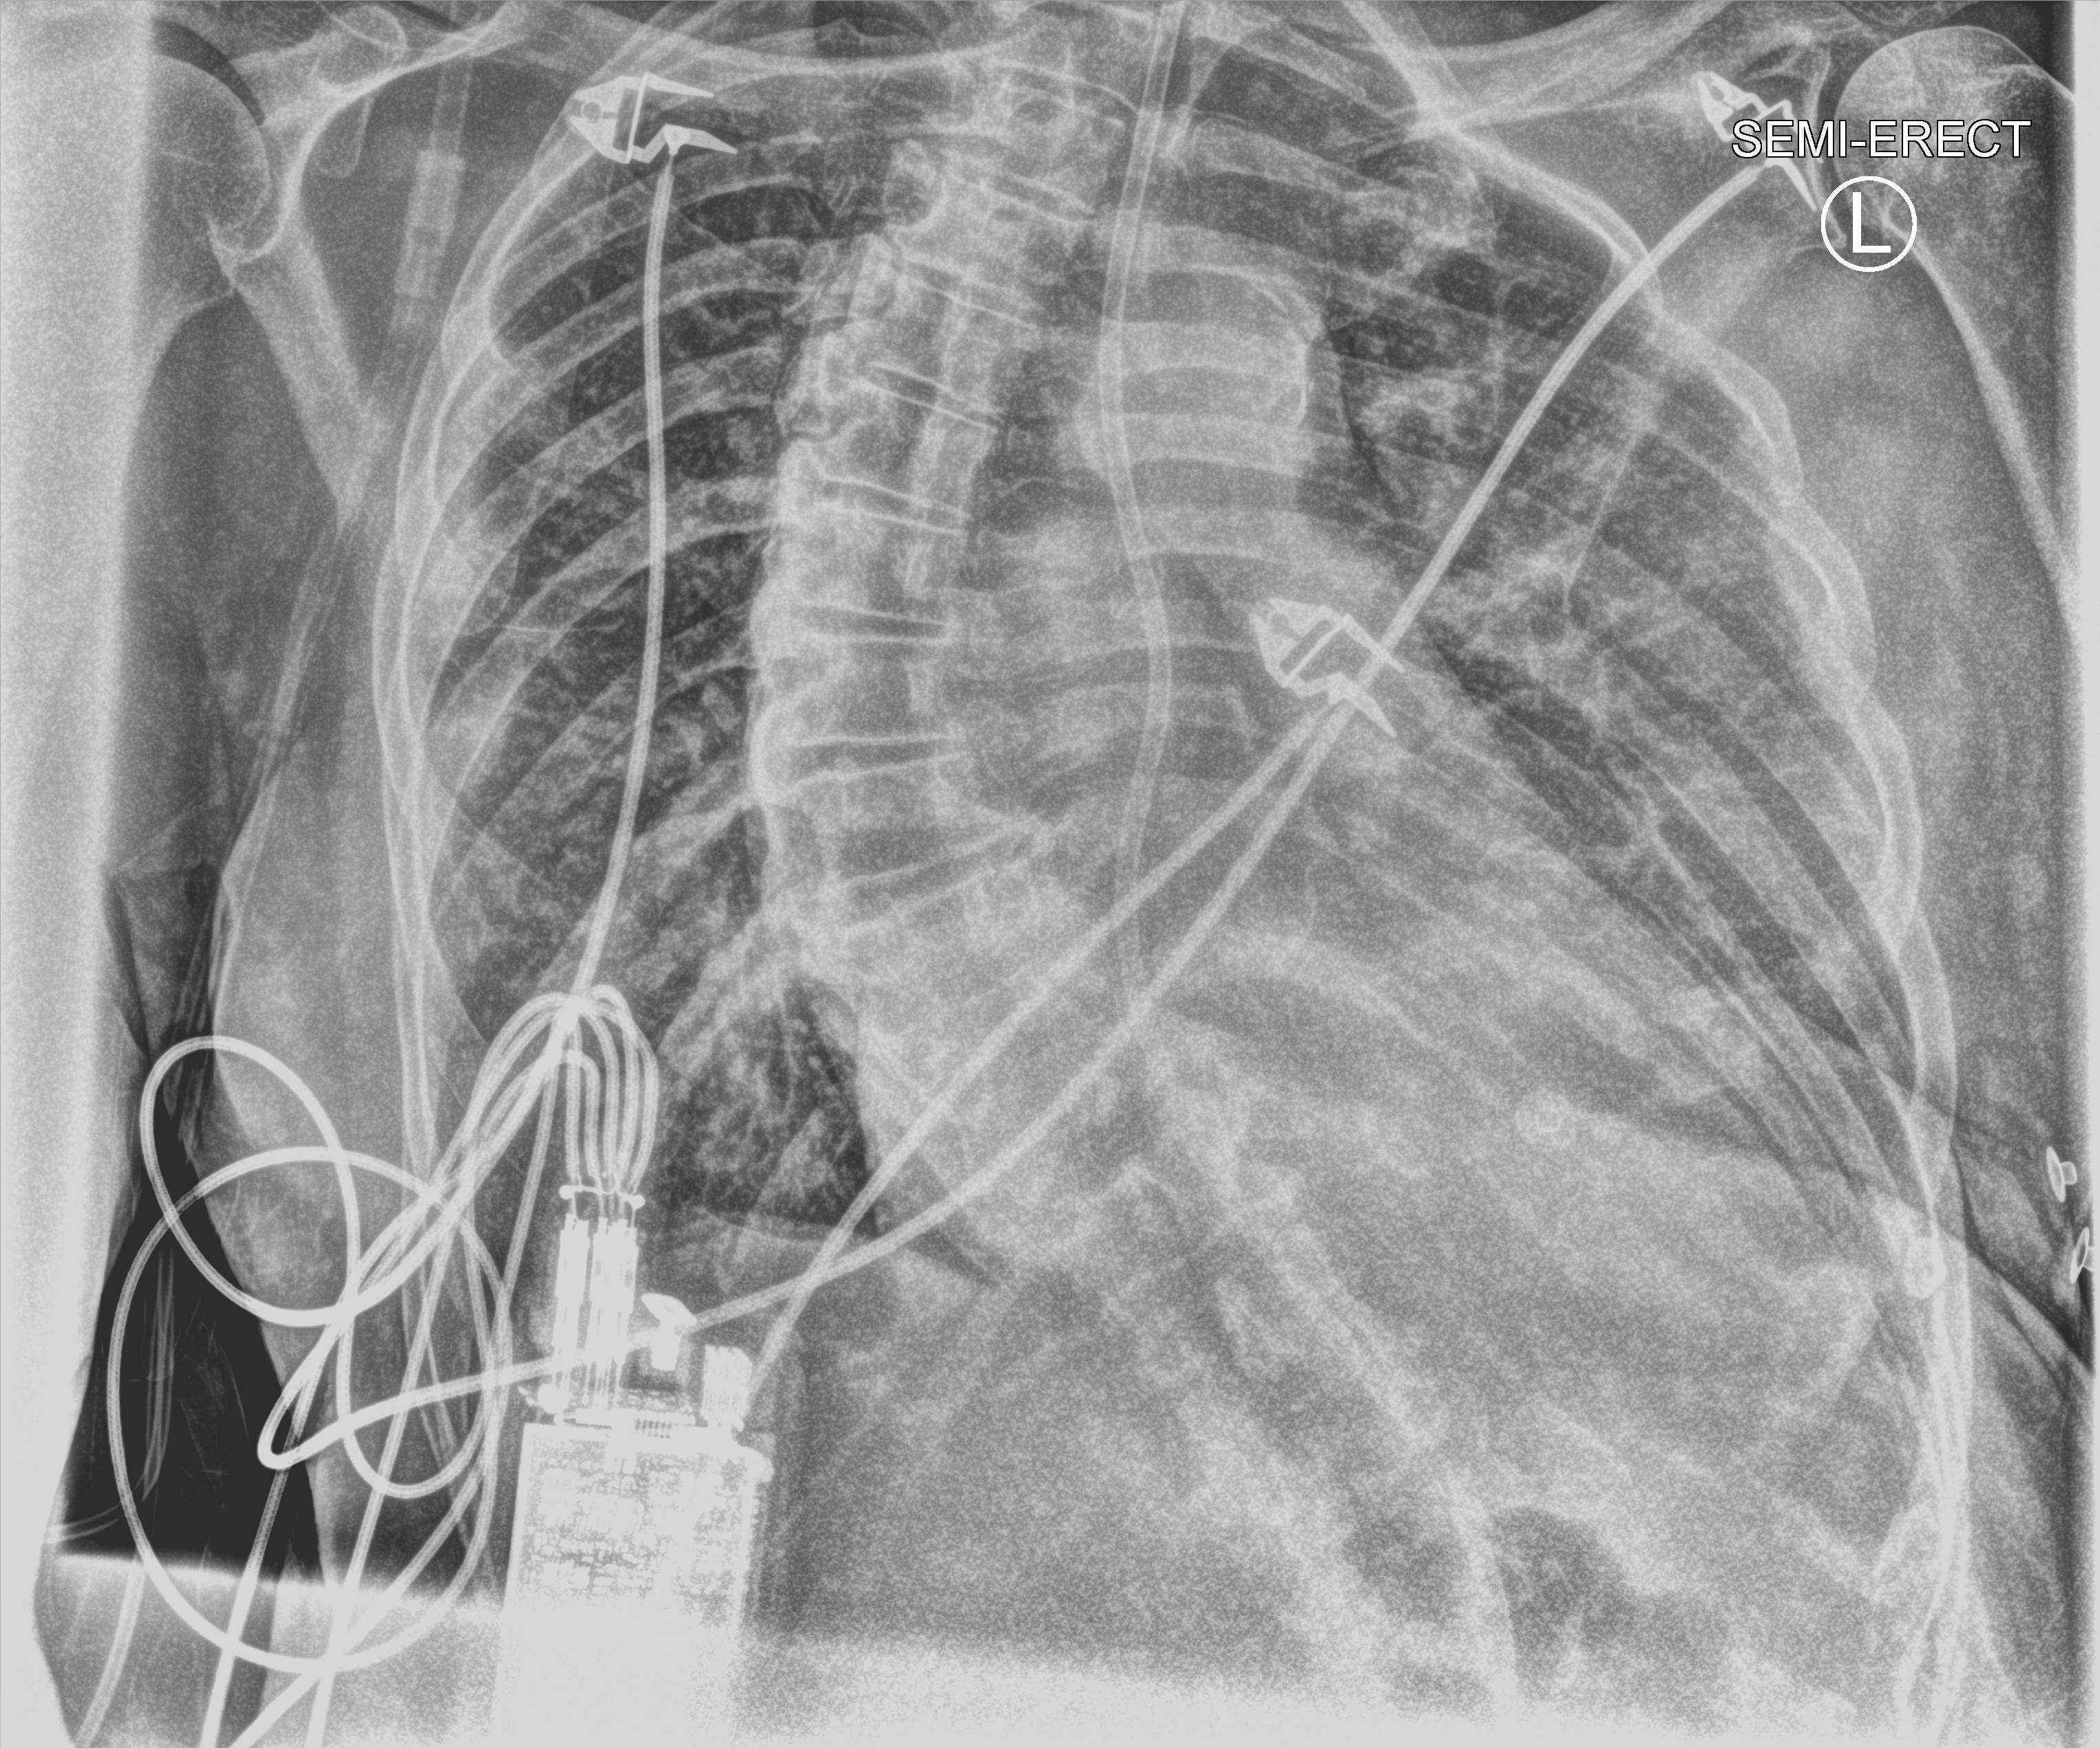
Bedside chest radiograph (computed radiography); anteroposterior (AP) projection. Patient hospitalised with COVID-19; male, aged 75–90 years.
Admission-level facts for this patient (not findings on this image; timing relative to this image not recorded): mechanically ventilated during this hospital stay: no; admitted to intensive care during this hospital stay: no.